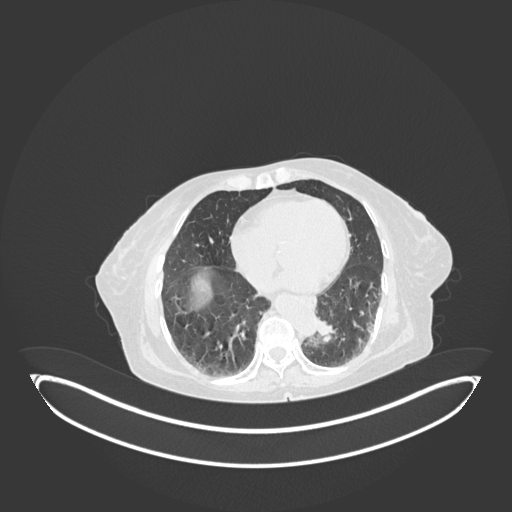
Chest CT, one axial slice. Slice 26 of 189 in the series (ordered by position). 120 kVp. Lung window (W 1500 / L -600 HU). 1 mm slice thickness. 512 × 512 image matrix, field of view 500 × 500 mm. Female patient, age 82 years. From the clinical record (not read from this slice): clinical TNM (as recorded): T1b N0 M1.
Outlined on this slice (rectangle marked by the reading radiologist):
- lung tumour (recorded histology: adenocarcinoma): box from (x=316, y=313) to (x=337, y=346) px